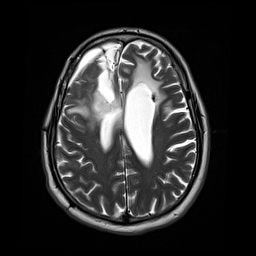
Brain MRI from a brain-tumour surgery series, one axial slice. Position 15 of 44 along the scan axis. 4 mm slice thickness. 256 × 256 image matrix, field of view 240 × 240 mm. Case-level facts recorded for this patient, not image findings: histopathology: Astrocytoma; WHO grade: 4; IDH mutation: yes; tumour location: Right Frontal.
Outlined on this slice (expert manual segmentation):
- tumour: bounding box (x1, y1, x2, y2) in pixels: (67, 89, 112, 124)